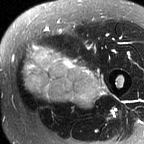
MRI of an extremity soft-tissue mass, one axial slice. Slice 23 of 60 in the series (ordered by position). T2-weighted fat-saturated. MR volume resampled by the dataset authors to the PET/CT grid (not the native acquisition matrix). 3.27 mm slice thickness. 144 × 144 image matrix, field of view 141 × 141 mm. Female patient. Case-level facts recorded for this patient, not image findings: histological type: pleiomorphic leiomyosarcoma; grade: intermediate; site of the primary tumour: left thigh.
Structures marked on this image (expert contour drawn on MRI and transferred to this co-registered scan by the dataset authors):
- gross tumour volume including surrounding oedema: bounding box [x1, y1, x2, y2] px = [20, 44, 108, 107]
- gross tumour volume (mass): [22, 44, 101, 105]